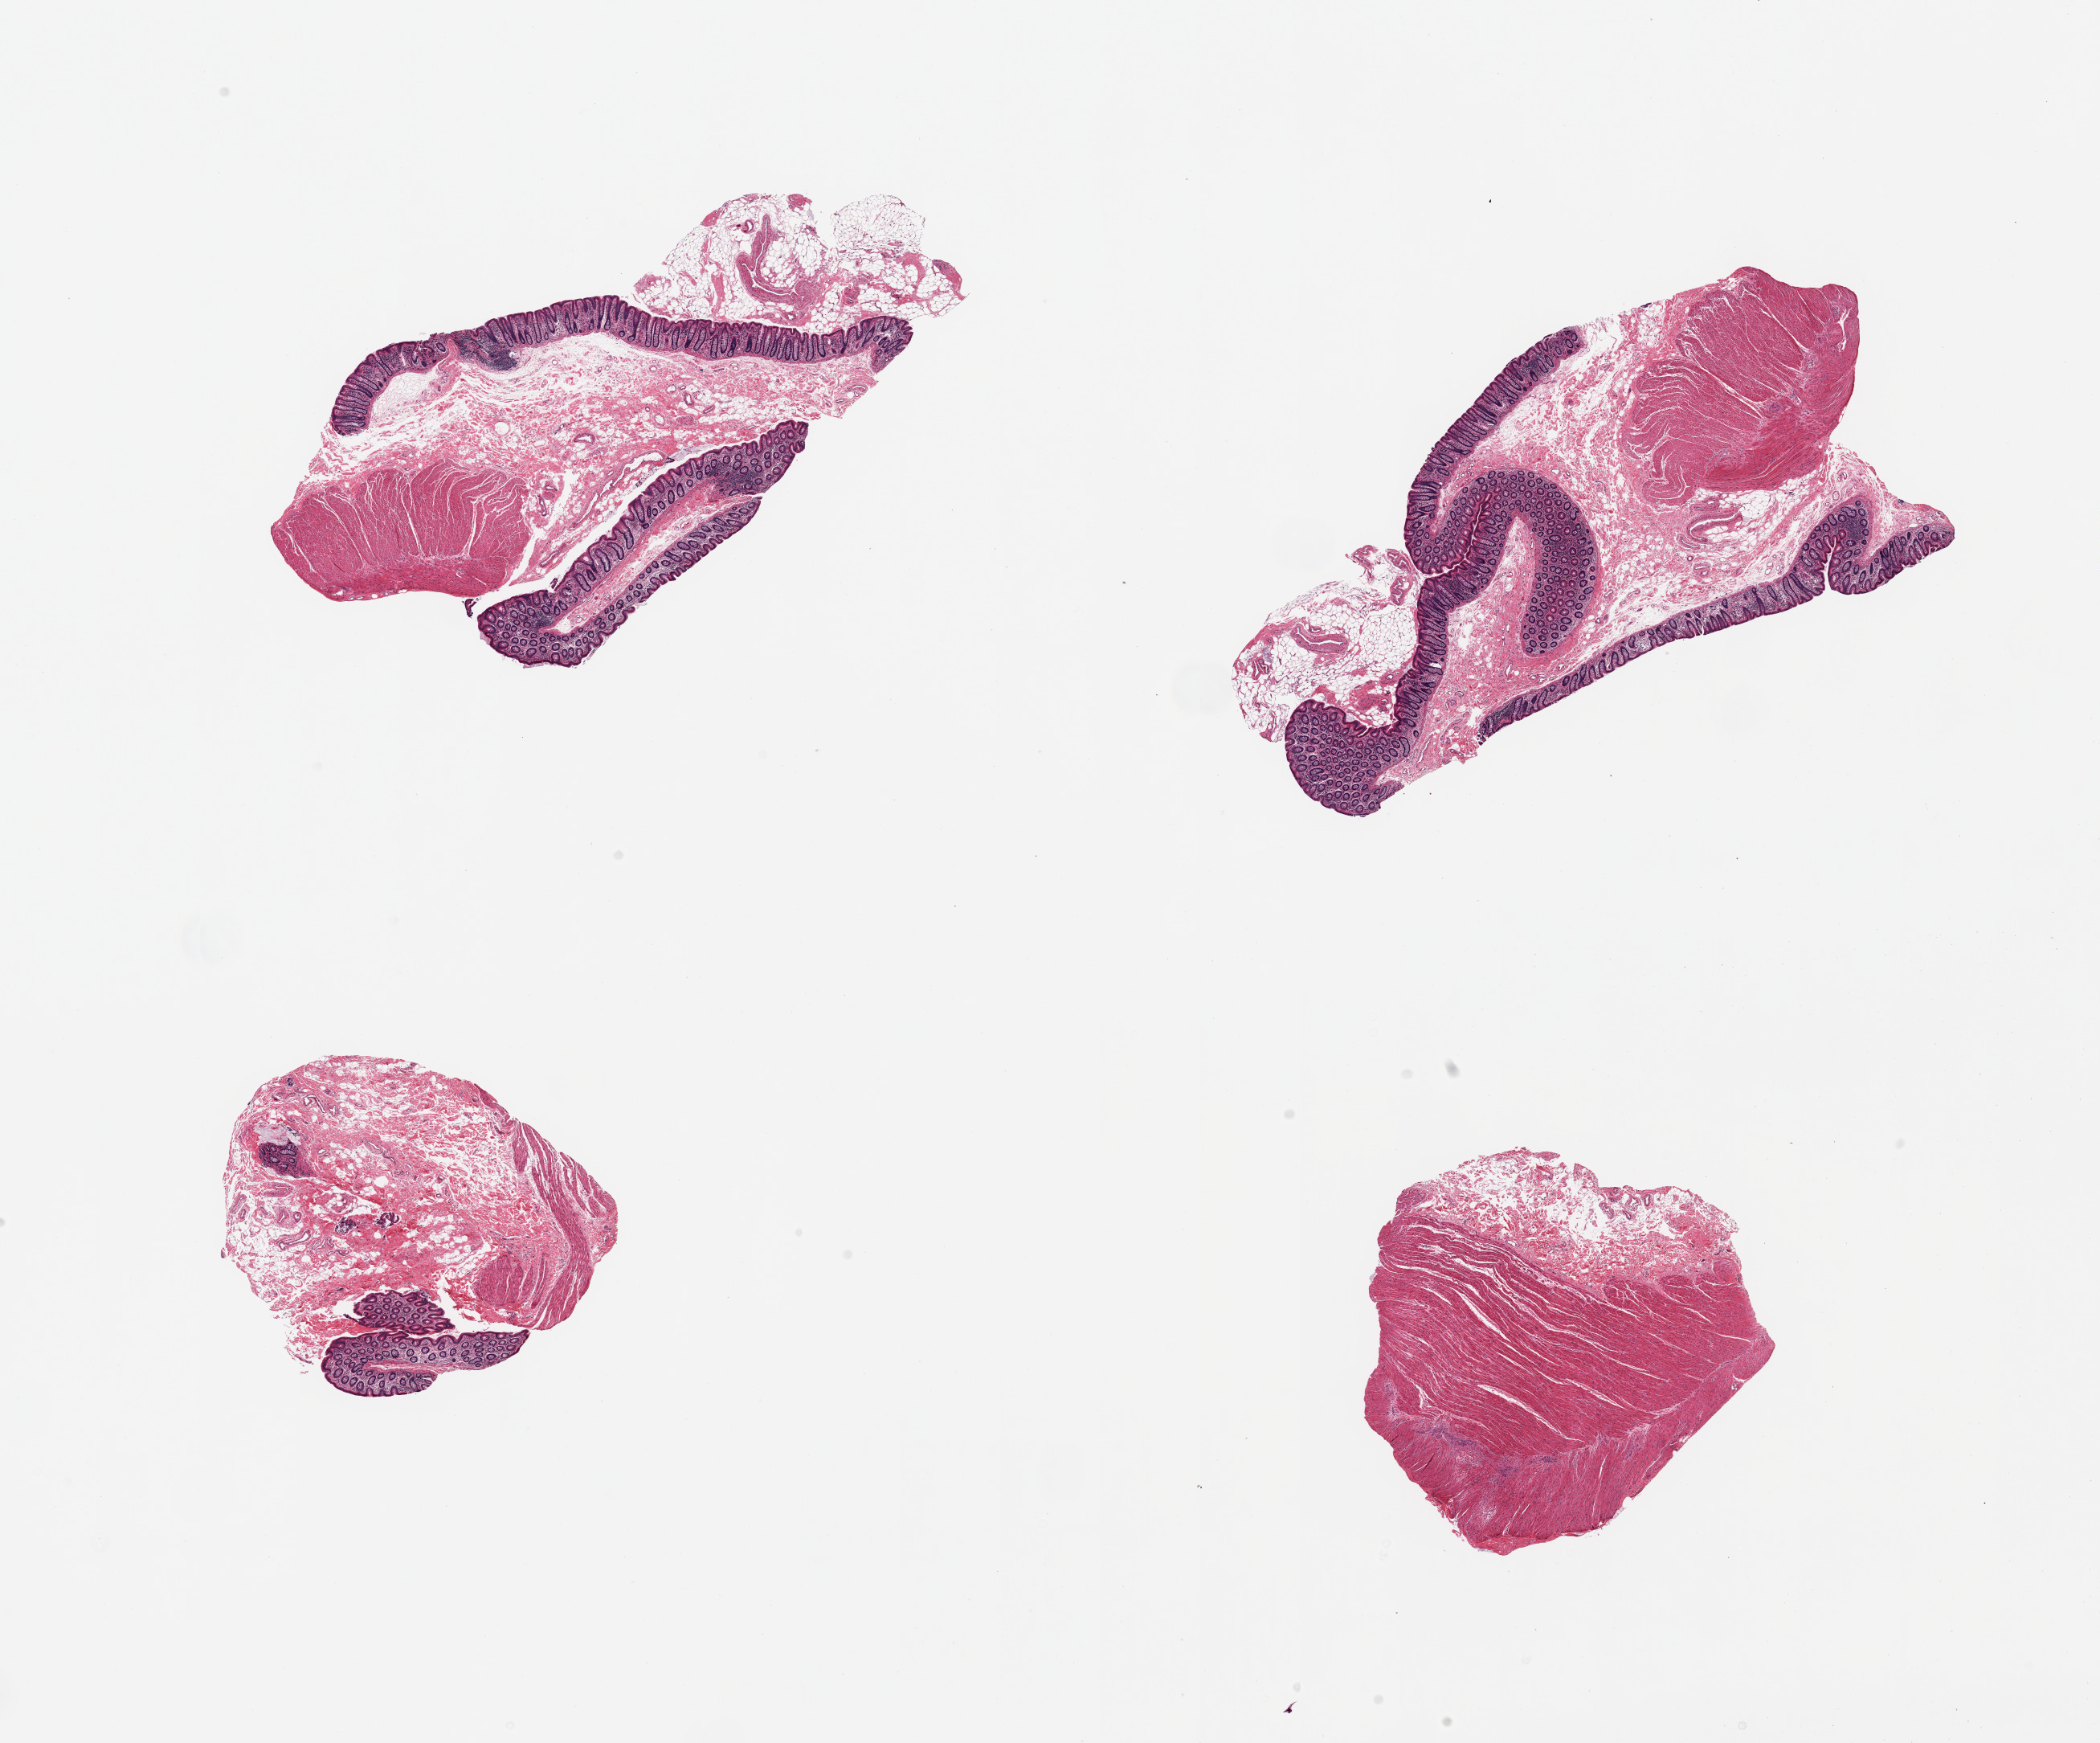
Whole-slide image, H&E stain, brightfield — low-resolution overview of the scanned area, about 20.7 x 17.2 mm (acquisition: 20x scan), PAXgene-fixed, paraffin-embedded tissue, sampled site (target tissue): transverse colon, donor tissue sample. Male donor.
• review note (as recorded): 4 pieces; 1 piece has no mucosa, 1 piece is mainly submucosa